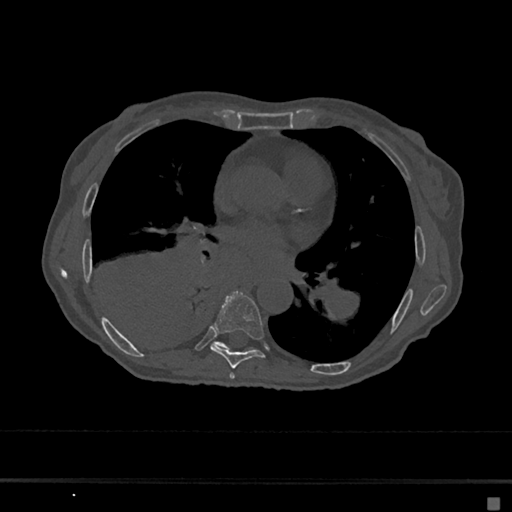
CT including the spine, one axial slice; 120 kVp; bone window (W 1800 / L 400 HU); 512 × 512 image matrix. Patient: female, 68 years. From the clinical record (not read from this slice): primary cancer: renal.
Outlined on this slice (semi-automatically segmented with operator editing):
- T6 vertebra: bounding box (x1, y1, x2, y2) in pixels: (229, 373, 235, 379)
- T7 vertebra: (210, 292, 266, 368)
- T8 vertebra: (215, 342, 254, 350)